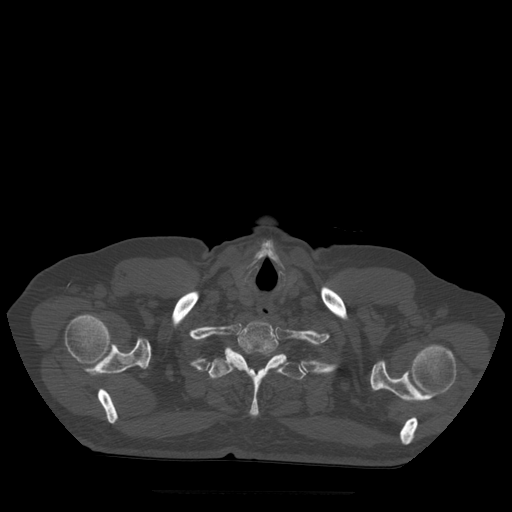
CT including the spine, one axial slice; slice 433 of 522 in the series (ordered by position); bone window (W 1800 / L 400 HU); 1.25 mm slice thickness; 512 × 512 image matrix, field of view 420 × 420 mm. Patient age 72 years. From the clinical record (not read from this slice): primary cancer: prostate.
Annotated regions visible in this slice (semi-automatic segmentation, software-assisted and operator-edited):
- T1 vertebra: box from (x=227, y=321) to (x=279, y=361) px
- T2 vertebra: (x=209, y=348)–(x=306, y=417)